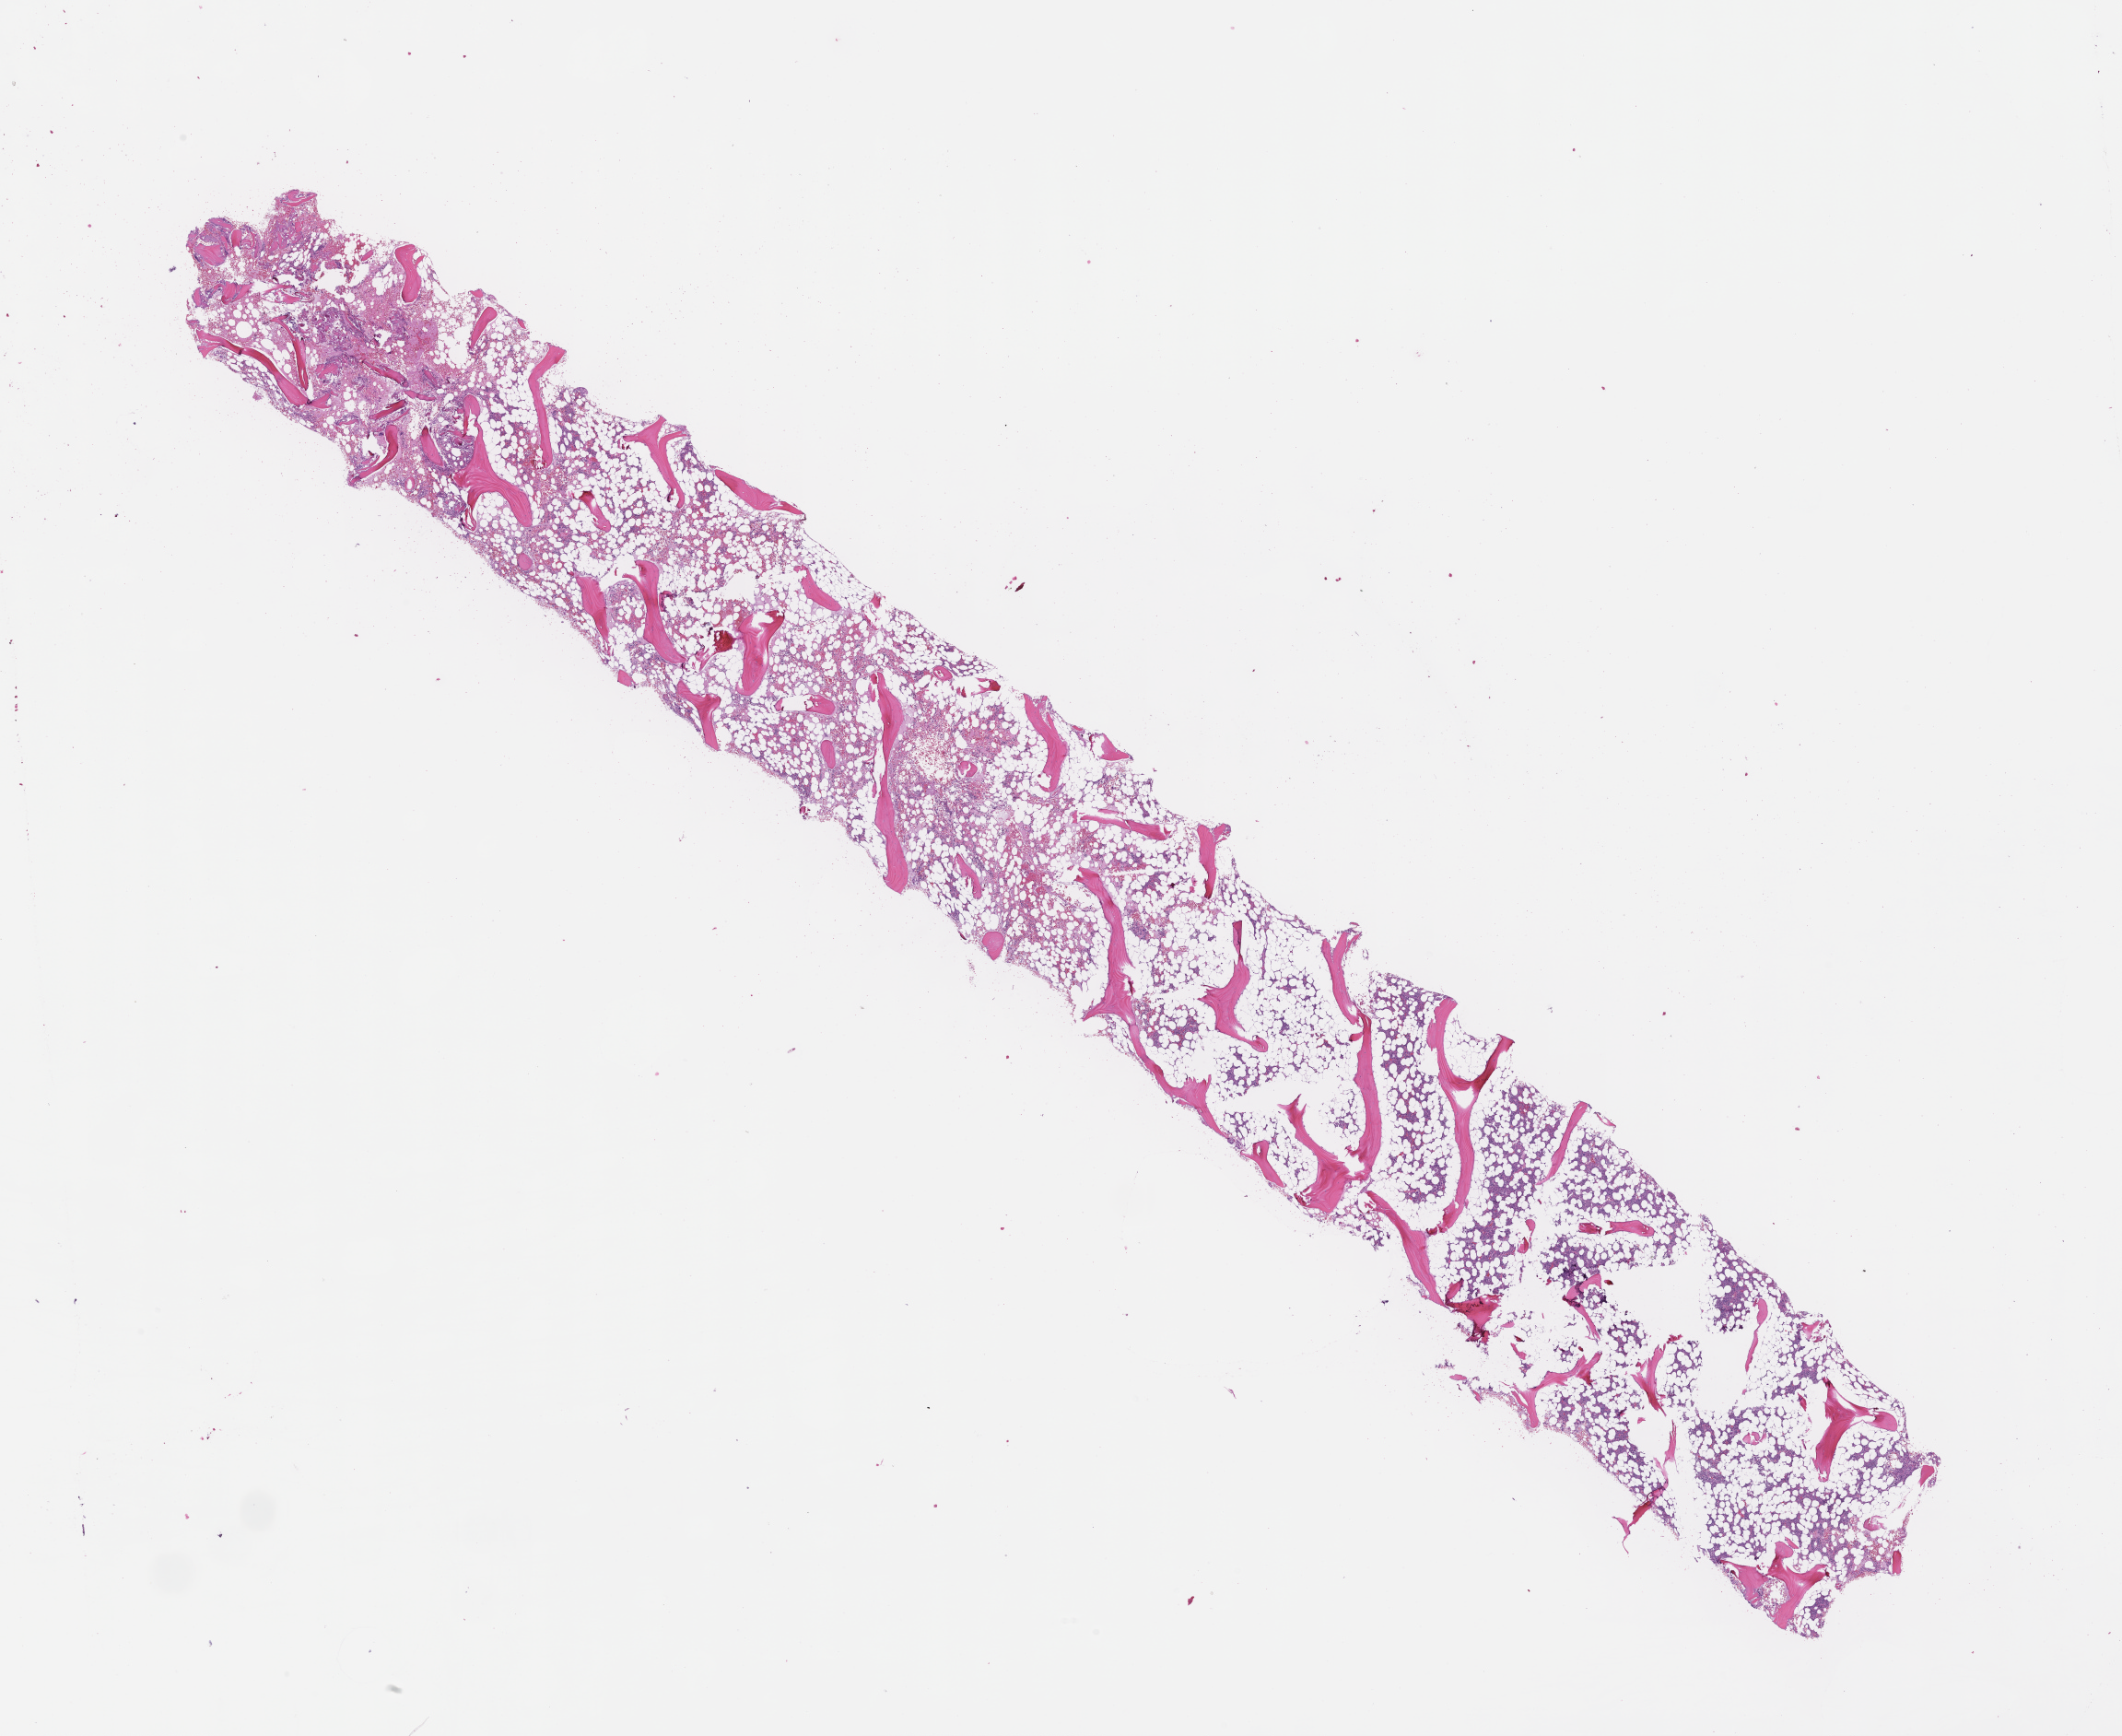
Digitized haematoxylin and eosin-stained section — shown as a low-resolution overview of the whole scanned area (about 18.6 x 15.2 mm), formalin-fixed paraffin-embedded section, tissue site: bone marrow, archival tissue. Male patient.
This section: primary tumour tissue. Diagnosis: Plasma Cell Myeloma.